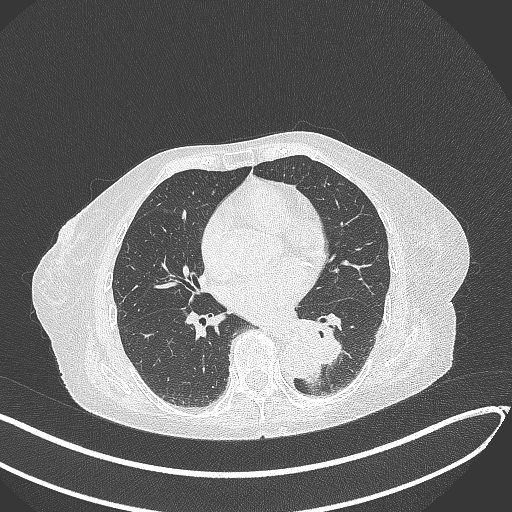
Chest CT, one axial slice; position 113 of 324 along the scan axis; reconstruction kernel B70f; 120 kVp; lung window (W 1500 / L -600 HU); 1 mm slice thickness; 512 × 512 image matrix, field of view 400 × 400 mm. Patient: female, 82 years. From the clinical record (not read from this slice): clinical TNM (as recorded): T1b N0 M1.
Outlined on this slice (bounding box drawn by a radiologist):
- lung tumour (recorded histology: adenocarcinoma): box from (x=292, y=315) to (x=343, y=368) px